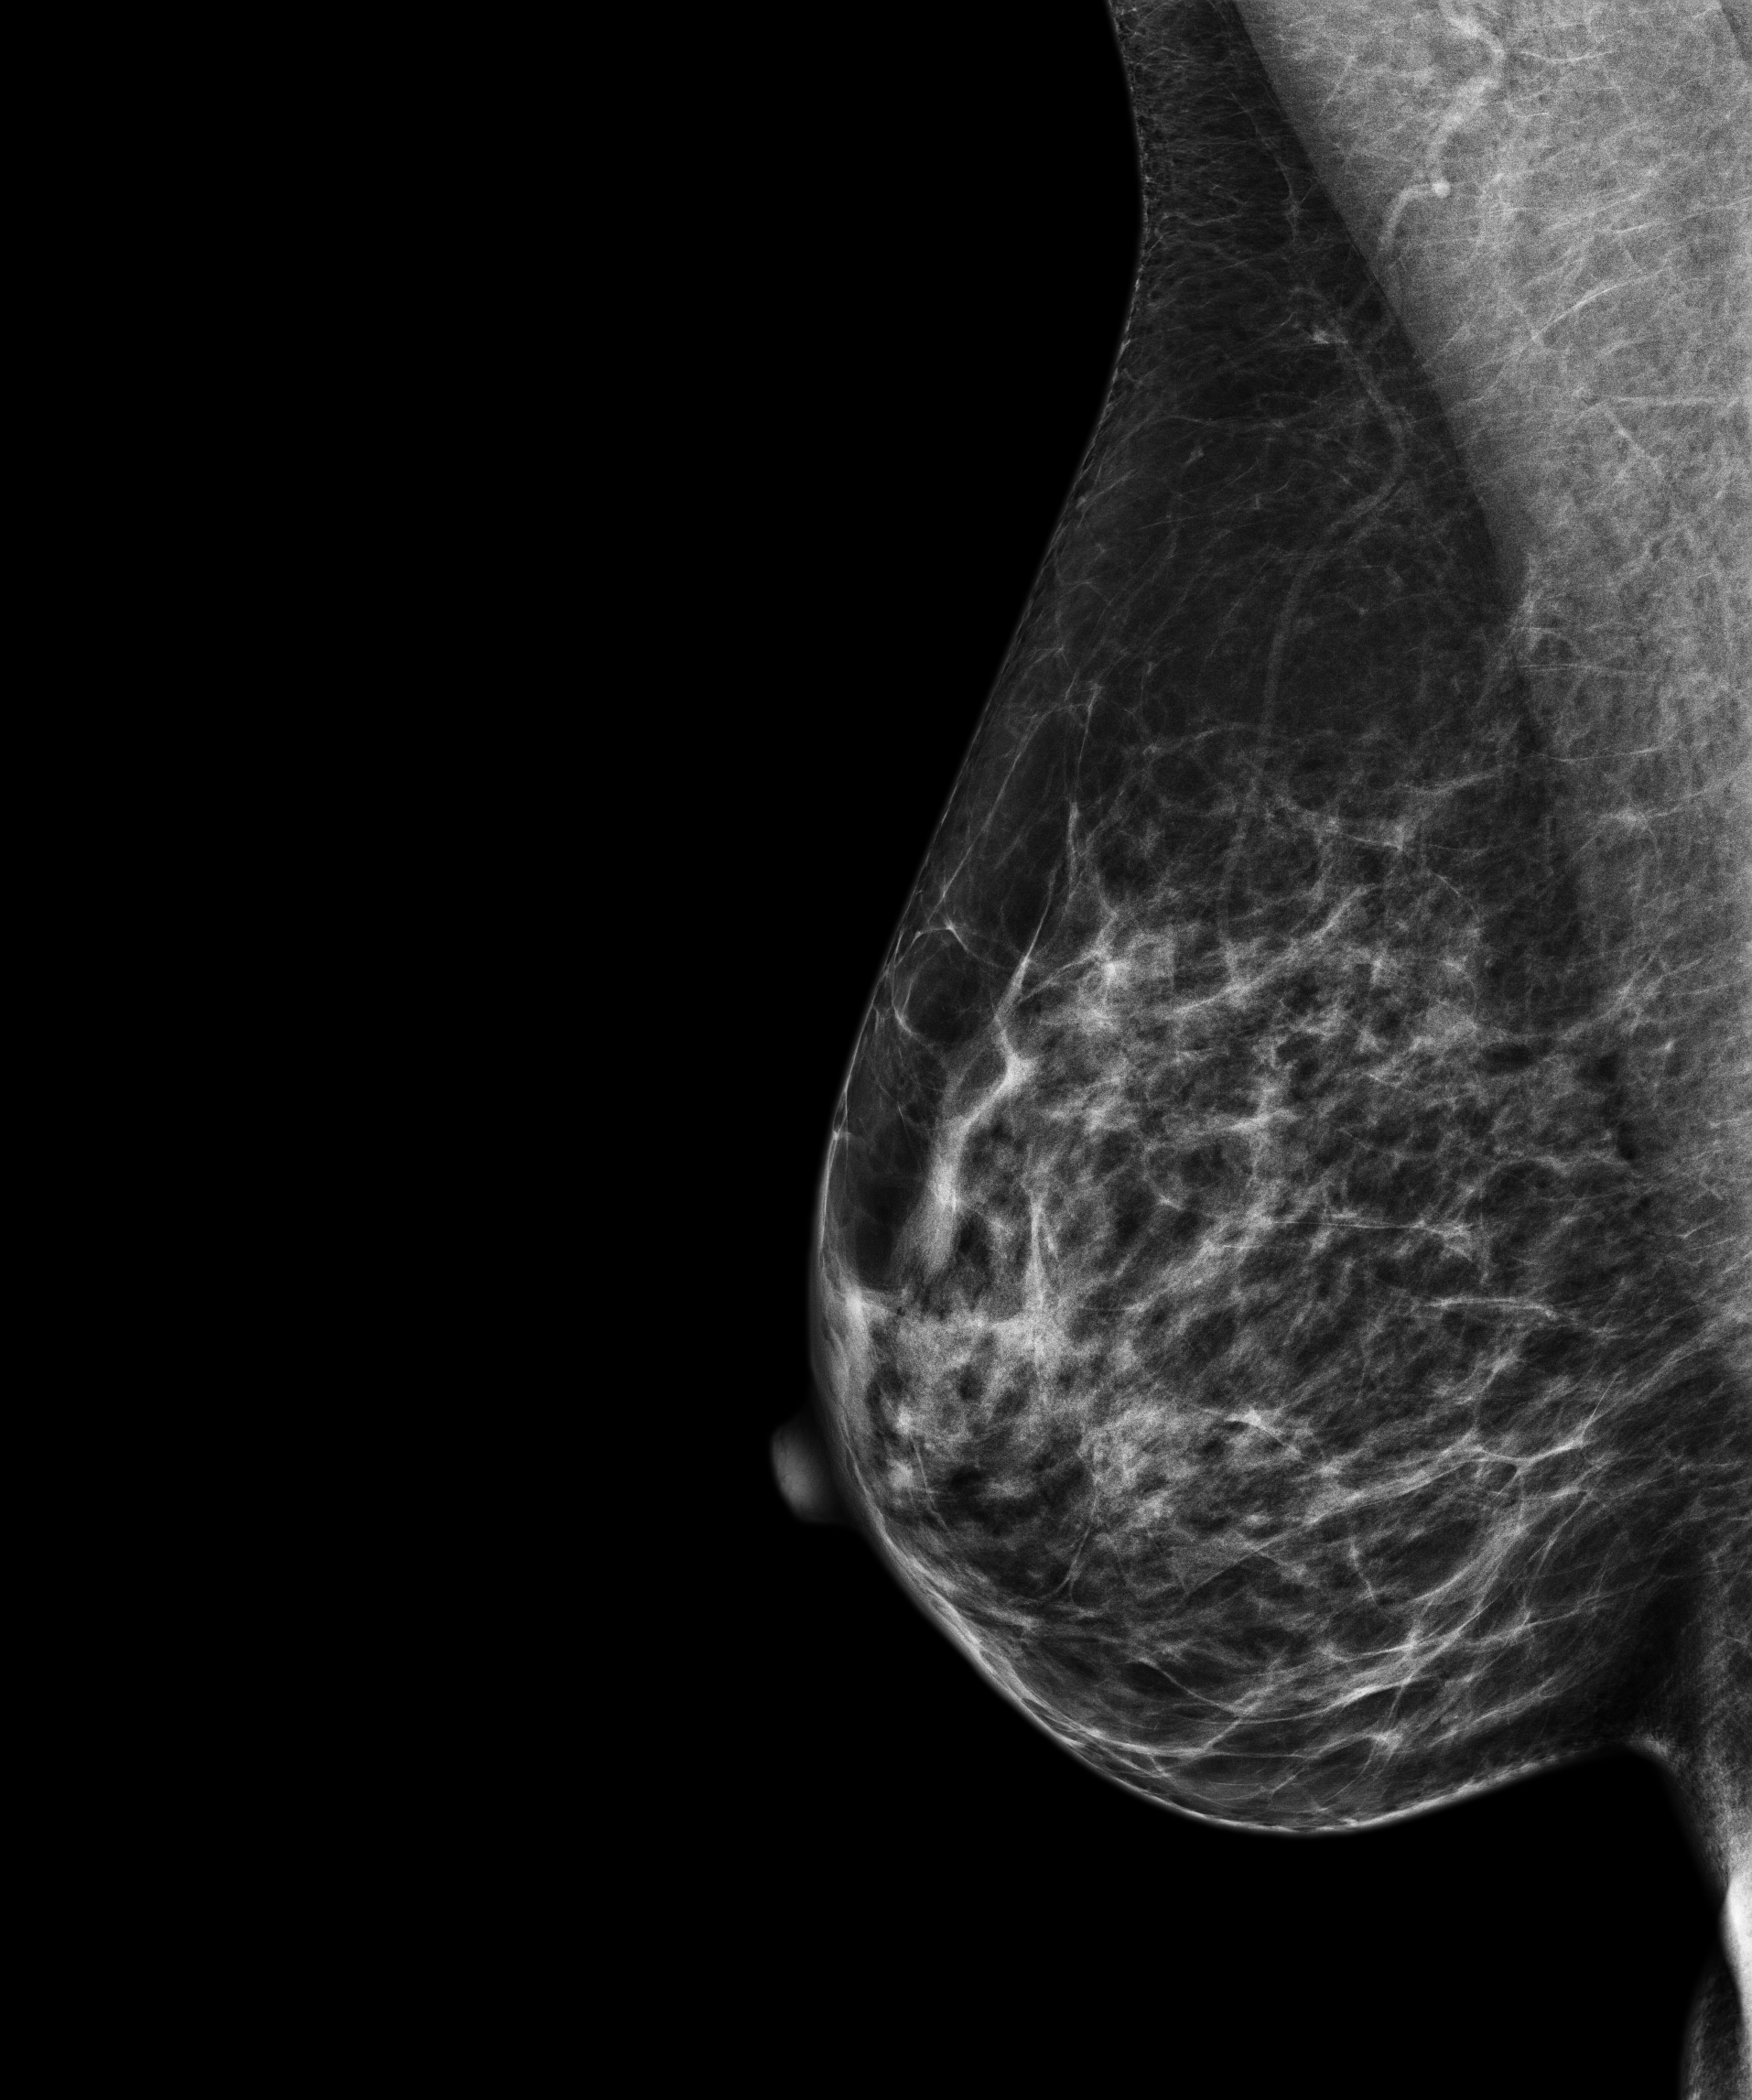
Screening examination, compressed breast thickness 55.8 mm, system: Senographe Pristina. Patient: female, 57 years.
Image type: full-field digital mammogram. Breast: right. Projection: mediolateral oblique (MLO) view.